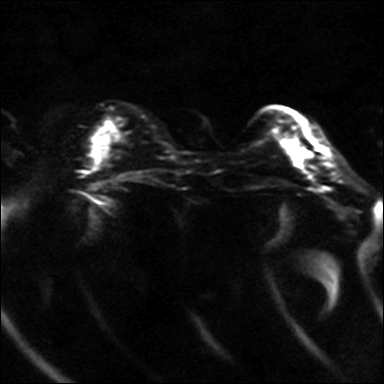
Breast MRI, one axial slice; position 9 of 36 along the scan axis; diffusion-weighted series; image 2 of 4 stored at this slice position (different b-values; order by instance number); 3 T; 4 mm slice thickness; 384 × 384 image matrix, field of view 320 × 320 mm. Female patient.
Annotated regions visible in this slice (expert manual segmentation):
- tumour on diffusion-weighted imaging: bounding box [x1, y1, x2, y2] px = [289, 147, 303, 159]